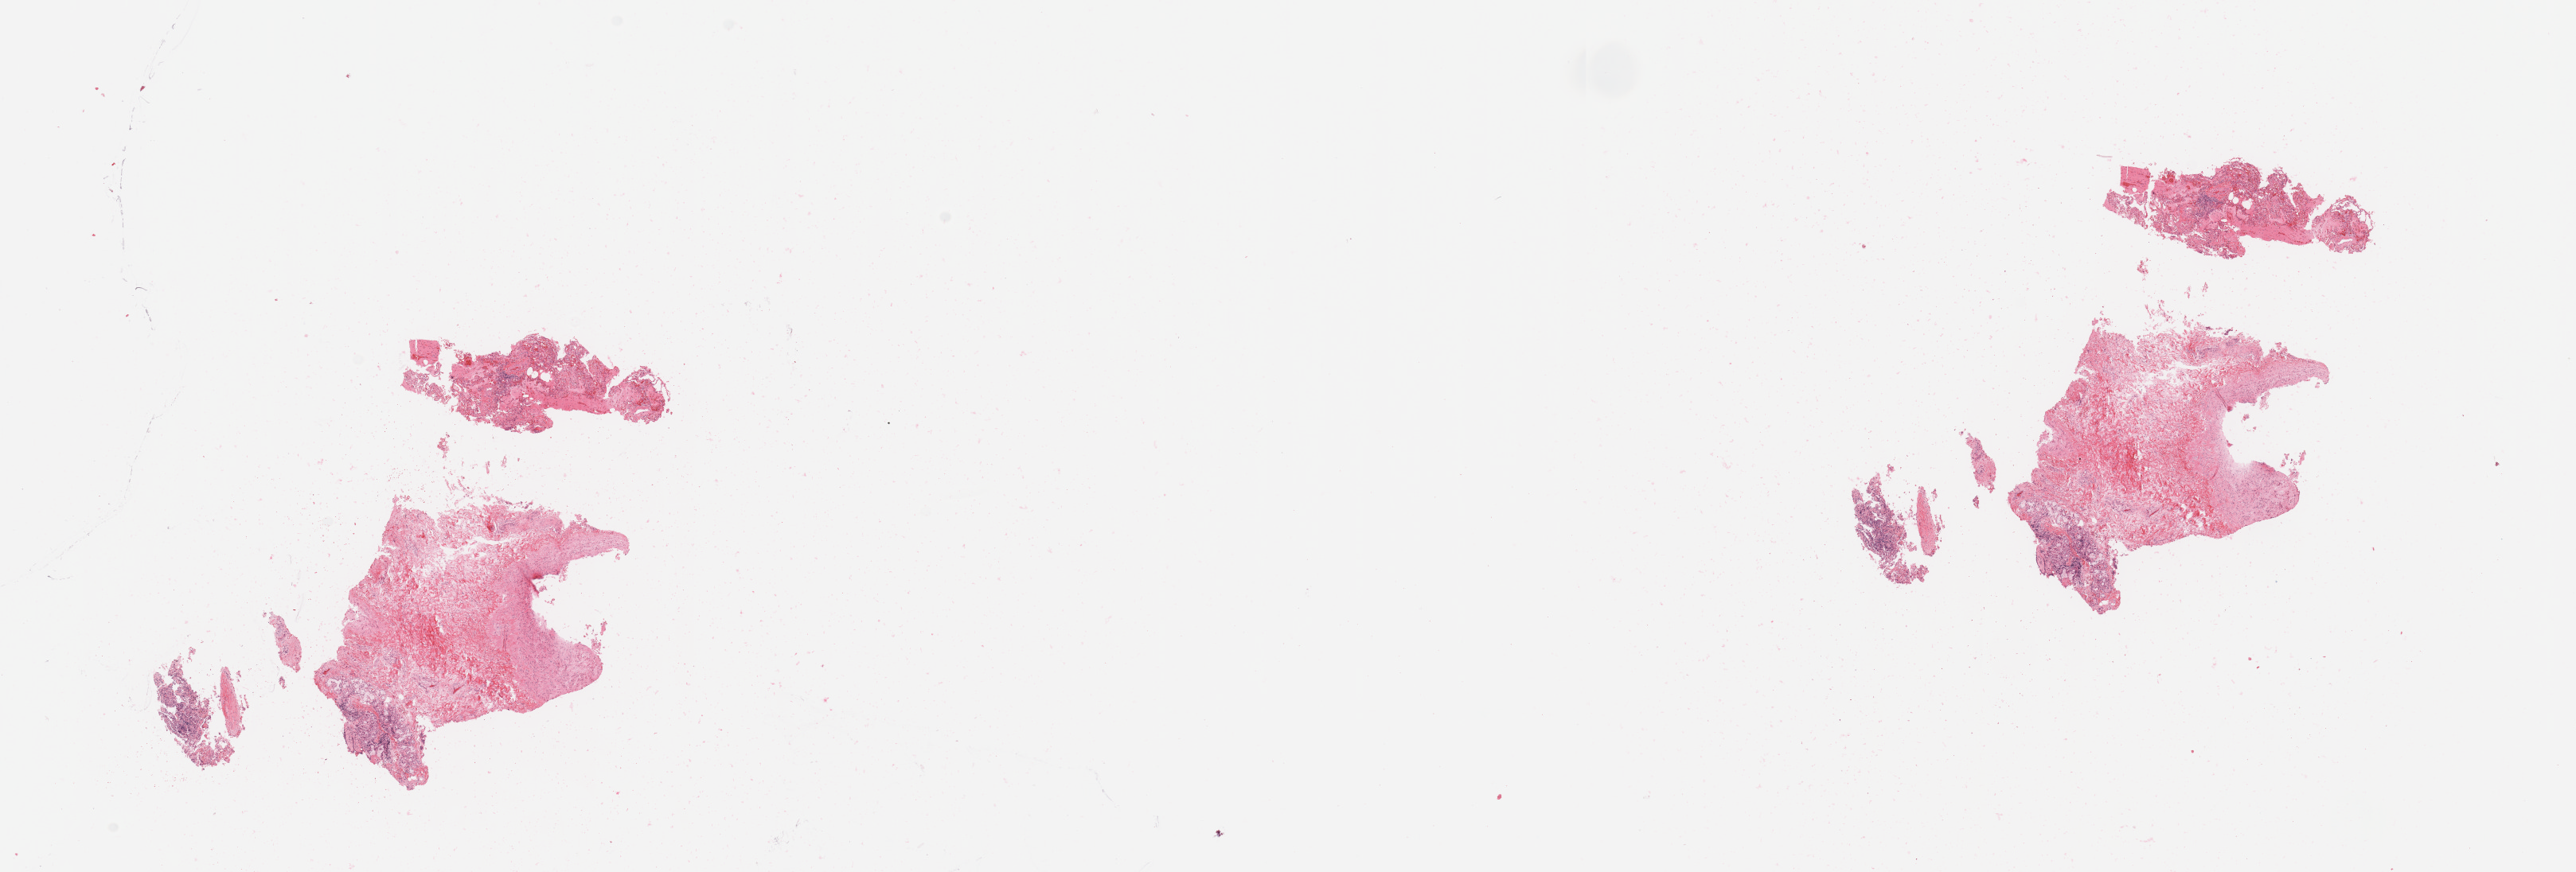
Digitized H&E tissue section (whole slide), a low-resolution overview of the entire scanned area, about 25.6 x 8.7 mm, normal (non-tumour) tissue sample, sampled site: lung. 47-year-old female patient.
• this section: normal (non-tumour) tissue from the same patient
• patient diagnosis: Adenocarcinoma, NOS